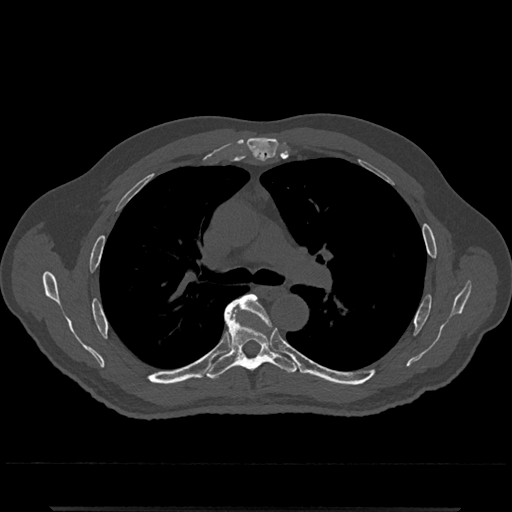
CT including the spine, one axial slice. Position 789 of 797 along the scan axis. Bone window (W 1800 / L 400 HU). 0.5 mm slice thickness. 512 × 512 image matrix, field of view 393 × 393 mm. Male patient, age 67 years. From the clinical record (not read from this slice): primary cancer: prostate.
Annotated regions visible in this slice (semi-automatic segmentation, software-assisted and operator-edited):
- T5 vertebra: box from (x=233, y=294) to (x=269, y=319) px
- T6 vertebra: (x=205, y=301)–(x=298, y=380)